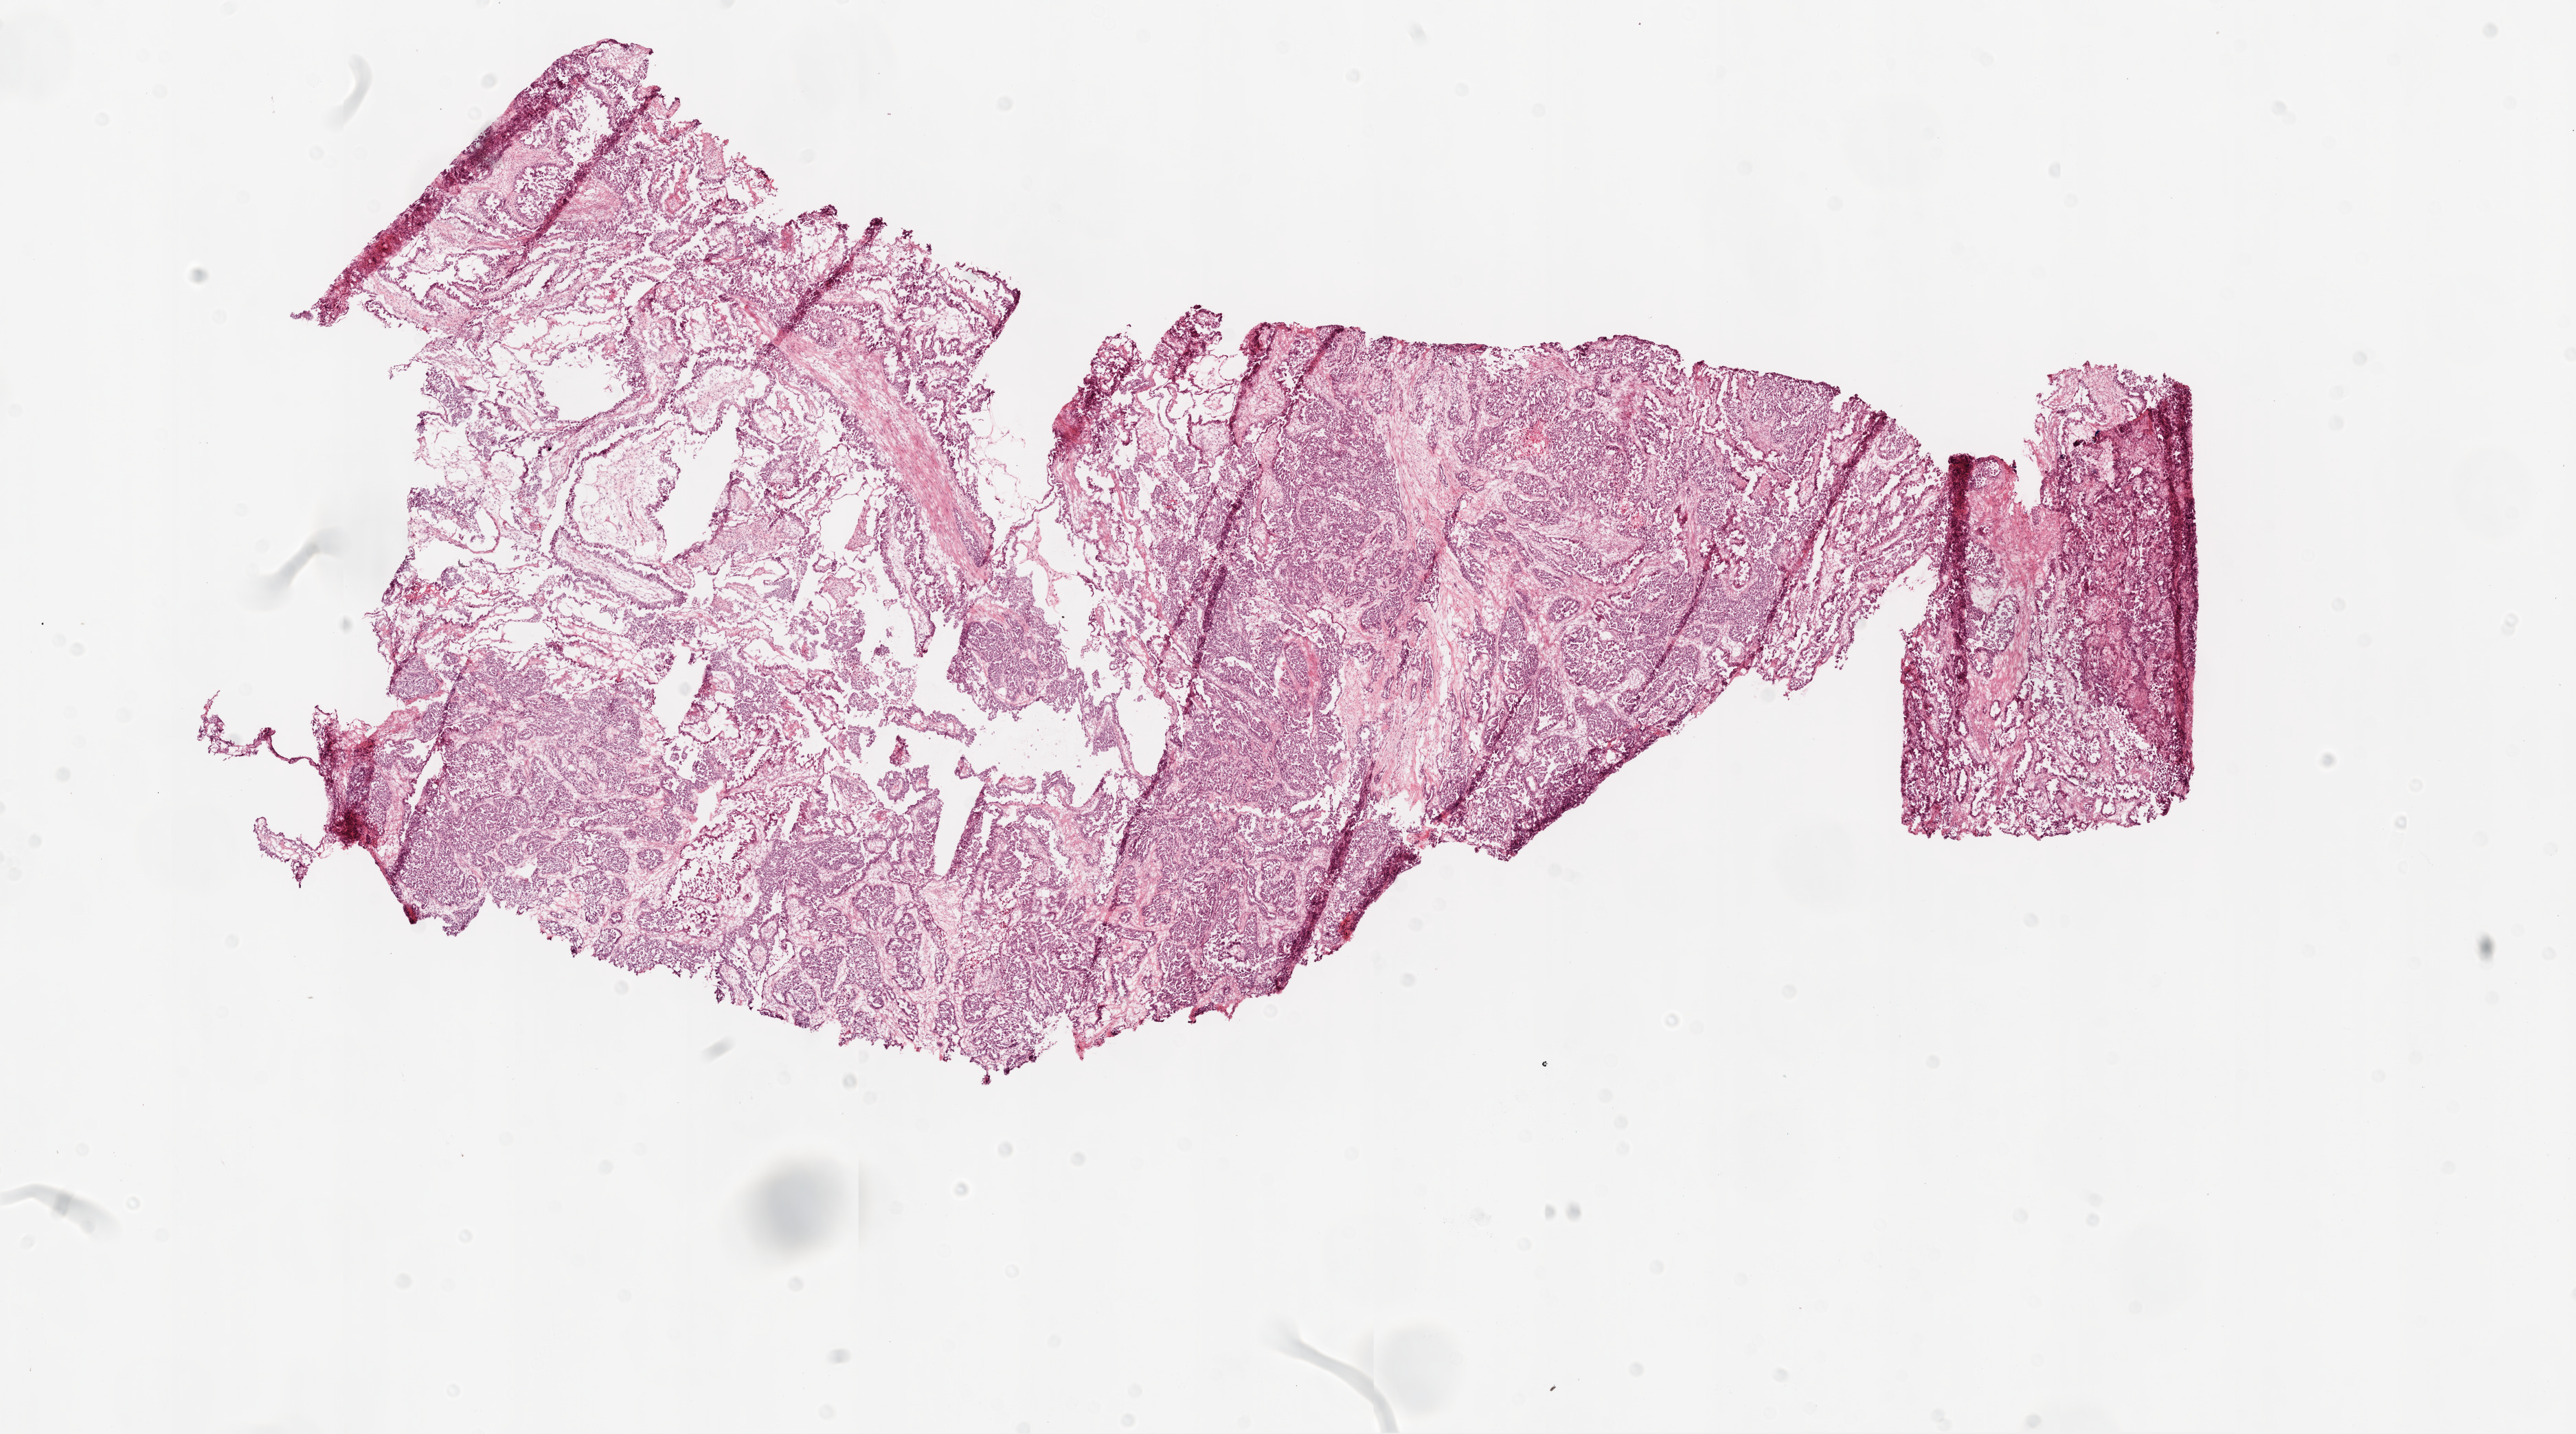
H&E whole-slide image, a low-resolution overview of the entire scanned area, about 15.0 x 8.4 mm, frozen section, ovary, primary tumour sample. Patient: female, age at initial diagnosis 56 years. Histologic grade: G3 (poorly differentiated). Slide review estimates, as recorded: tumour cells 90%, tumour nuclei 95%, normal cells 0%, stromal cells 10%, necrosis 0%.
- FIGO stage: IIIC
- laterality: bilateral
- histologic diagnosis: Serous cystadenocarcinoma, NOS